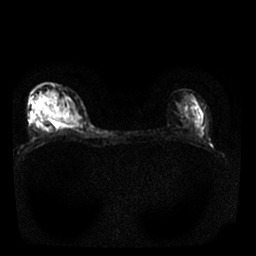
Breast MRI, one axial slice. Position 15 of 25 along the scan axis. Diffusion-weighted series; image 2 of 4 stored at this slice position (different b-values; order by instance number). 1.5 T. 256 × 256 image matrix, field of view 310 × 310 mm. Female patient.
Structures marked on this image (manually delineated by an expert):
- tumour on diffusion-weighted imaging: box from (x=42, y=113) to (x=78, y=125) px